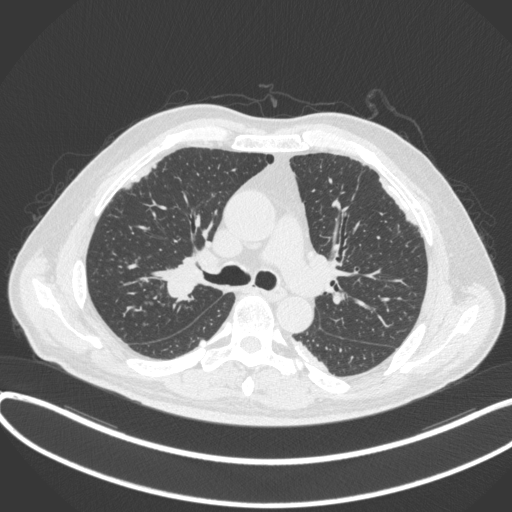
Chest CT, one axial slice. Position 269 of 455 along the scan axis. Lung window (W 1500 / L -600 HU). 1 mm slice thickness. 512 × 512 image matrix. Patient: male, 58 years. From the clinical record (not read from this slice): clinical TNM (as recorded): T1c N0 M0.
Outlined on this slice (bounding box drawn by a radiologist):
- lung tumour (recorded histology: squamous cell carcinoma): bounding box [x1, y1, x2, y2] px = [150, 254, 205, 304]